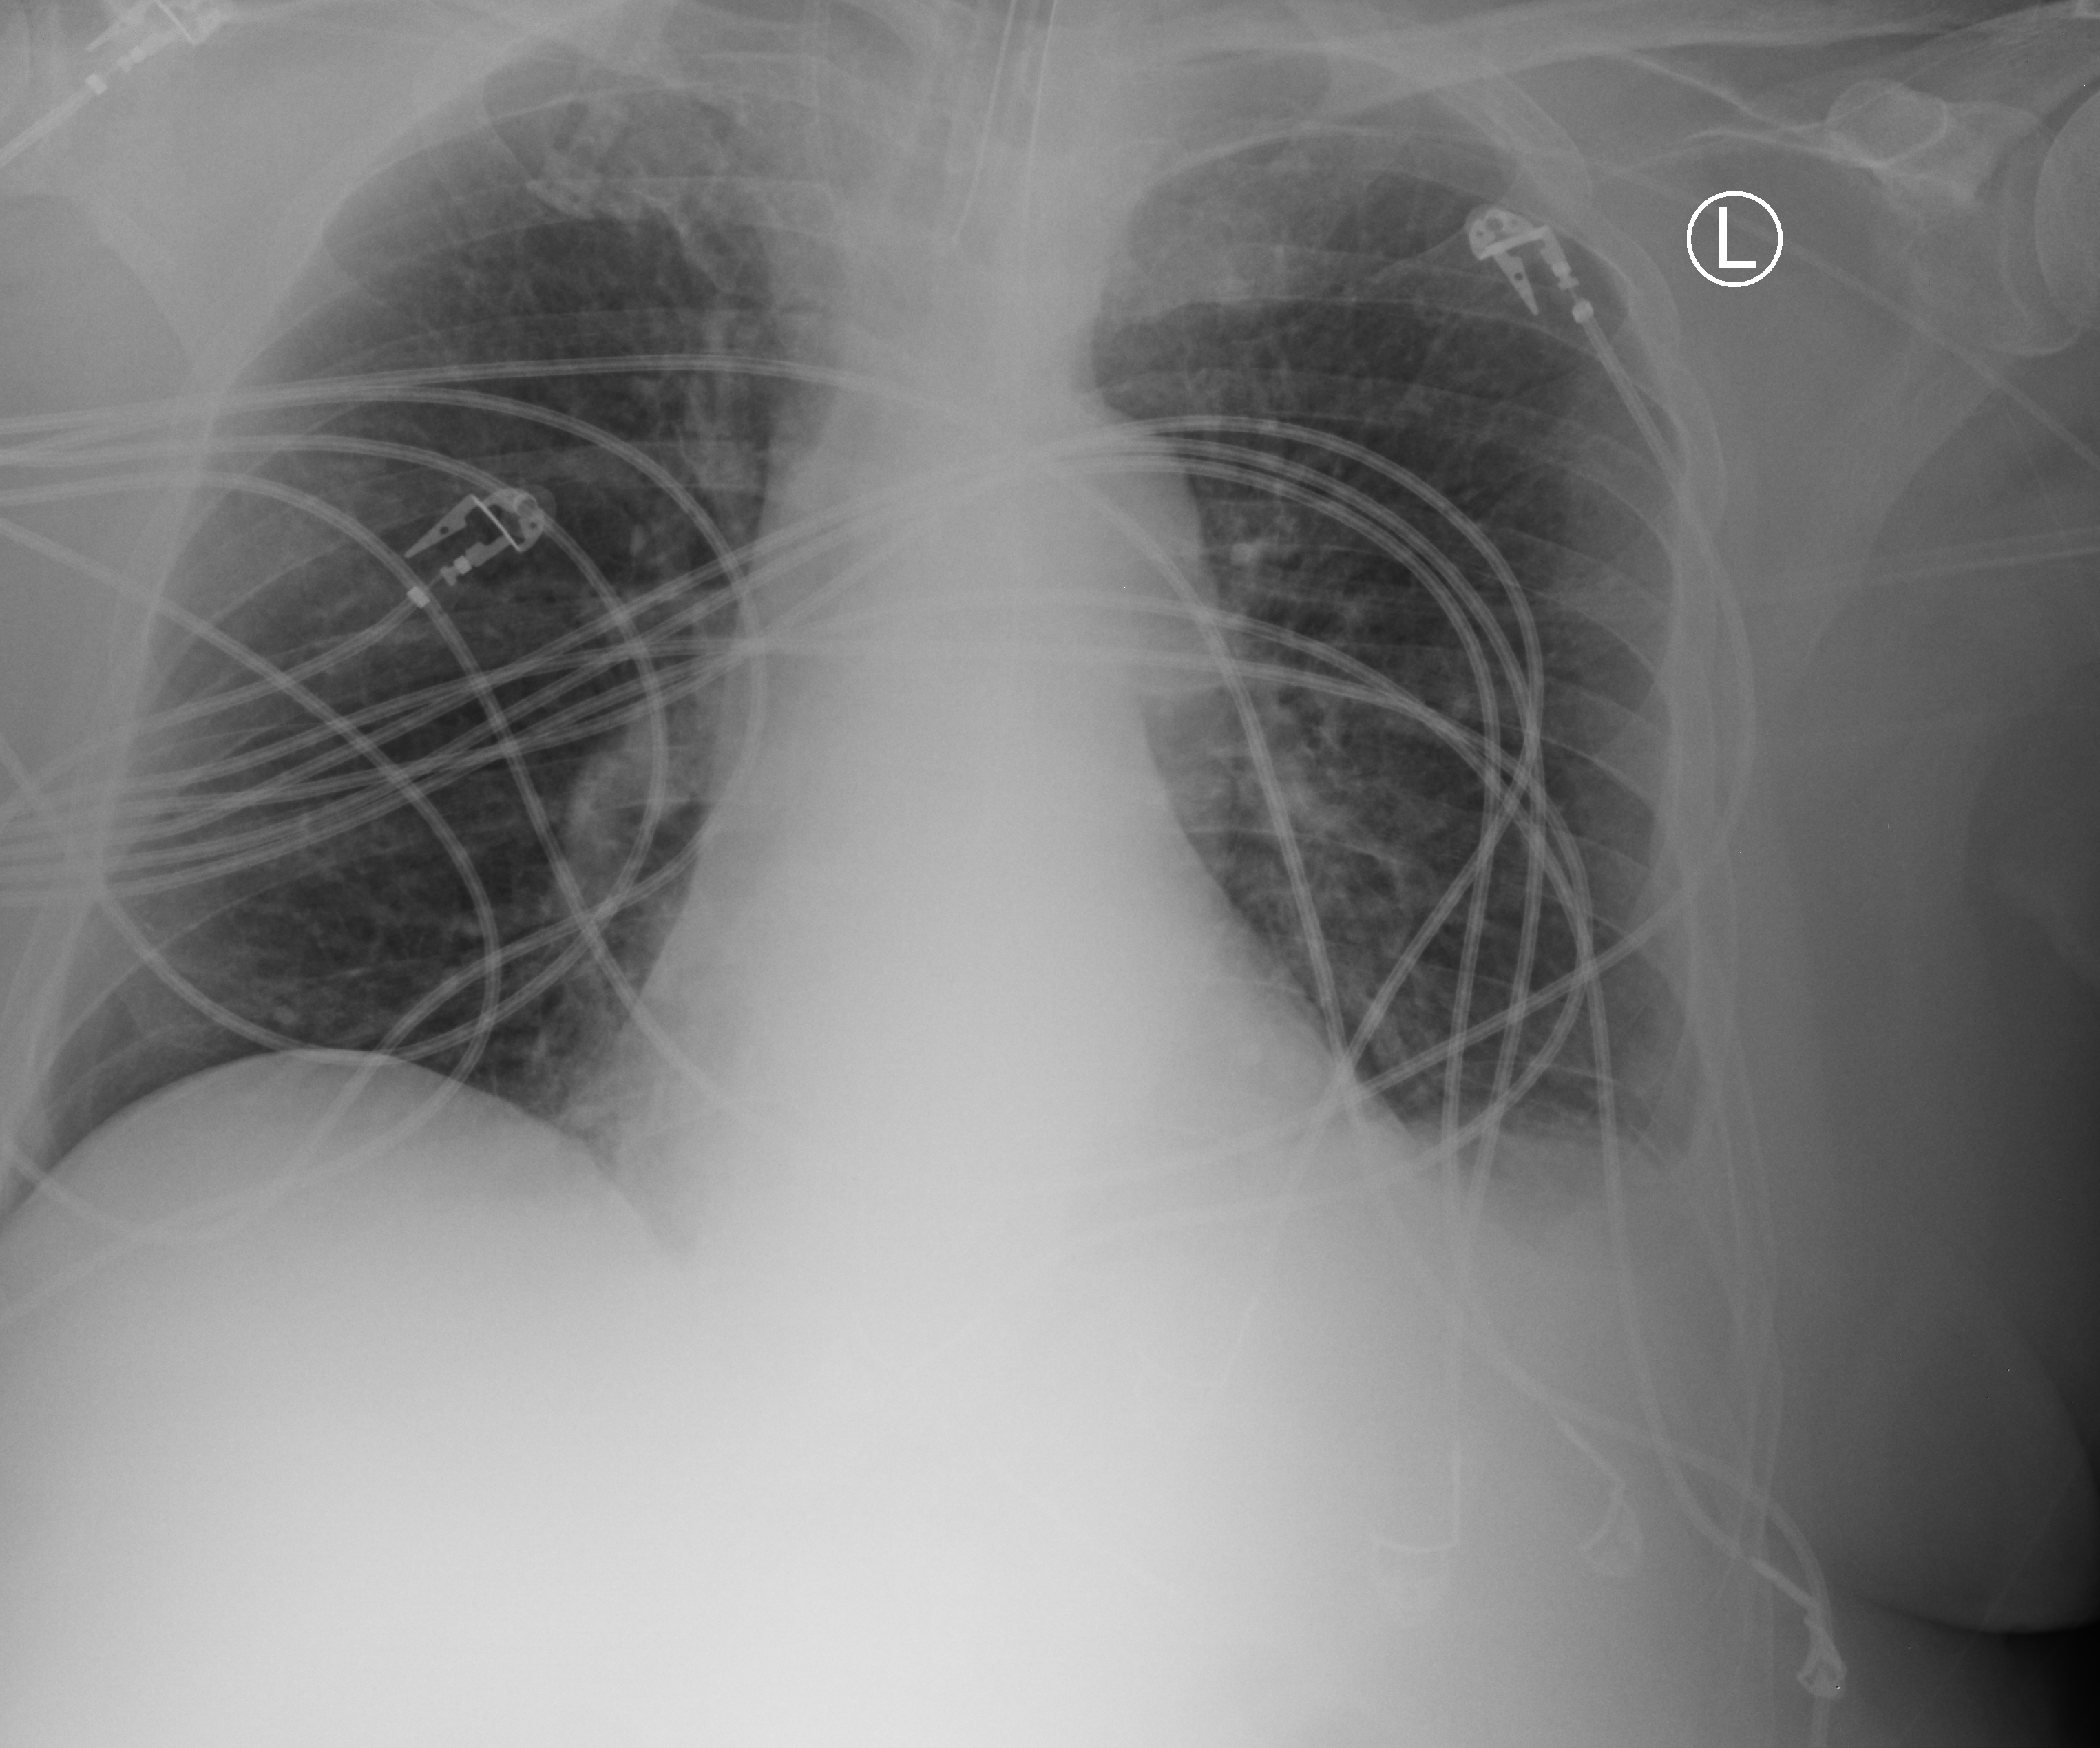
Portable chest radiograph, anteroposterior (AP) projection. Patient hospitalised with COVID-19; male, aged 60–74 years.
From the hospital-stay record, not from the radiograph (when in the stay this image was taken is not recorded): mechanically ventilated during this hospital stay: yes.